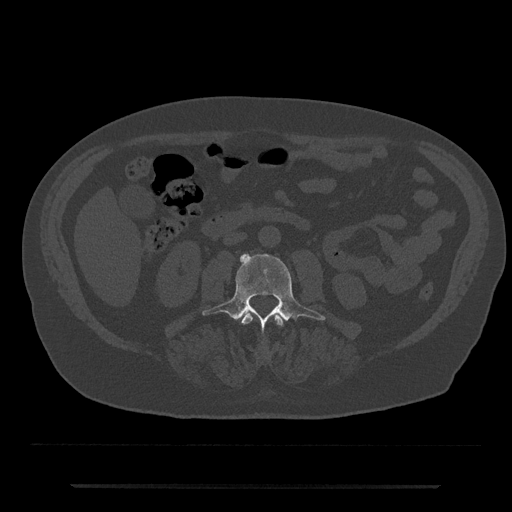
CT including the spine, one axial slice. Slice 420 of 797 in the series (ordered by position). Reconstruction kernel Br40s/3. 120 kVp. Bone window (W 1800 / L 400 HU). 0.5 mm slice thickness. 512 × 512 image matrix. Male patient, age 80 years. From the clinical record (not read from this slice): primary cancer: prostate; vertebrae with lytic lesions (as recorded): L1, T11.
Structures marked on this image (semi-automatic segmentation, software-assisted and operator-edited):
- L2 vertebra: bounding box <242,313,283,326> (left, top, right, bottom; pixels)
- L3 vertebra: <202,253,325,332>